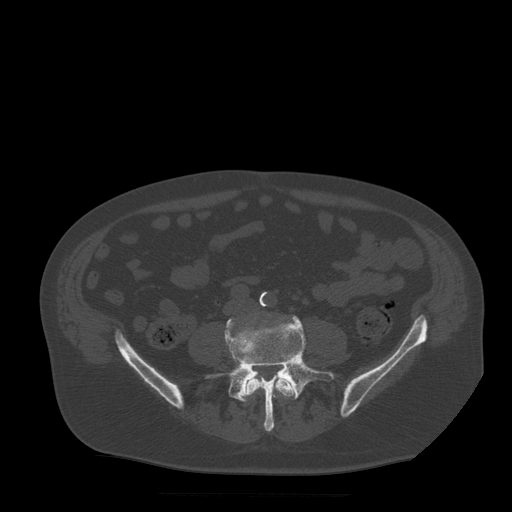
CT including the spine, one axial slice. Slice 97 of 522 in the series (ordered by position). Bone window (W 1800 / L 400 HU). 1.25 mm slice thickness. 512 × 512 image matrix, field of view 420 × 420 mm. Patient age 72 years. From the clinical record (not read from this slice): primary cancer: prostate.
Outlined on this slice (semi-automatic segmentation, software-assisted and operator-edited):
- L4 vertebra: bounding box [x1, y1, x2, y2] px = [242, 377, 297, 402]
- L5 vertebra: [209, 316, 336, 432]